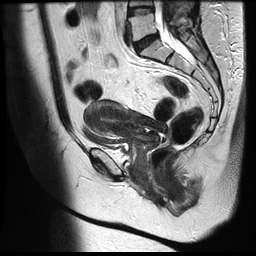
Pelvic MRI for cervical cancer, one sagittal slice; slice 15 of 35 in the series (ordered by position); T2-weighted; 1.5 T; TE 122.8 ms, TR 4992 ms; 4 mm slice thickness; 256 × 256 image matrix, field of view 300 × 300 mm. Female patient, age 42 years.
Outlined on this slice (outlined manually by an expert reader):
- uterus and cervix: box from (x=83, y=99) to (x=166, y=144) px